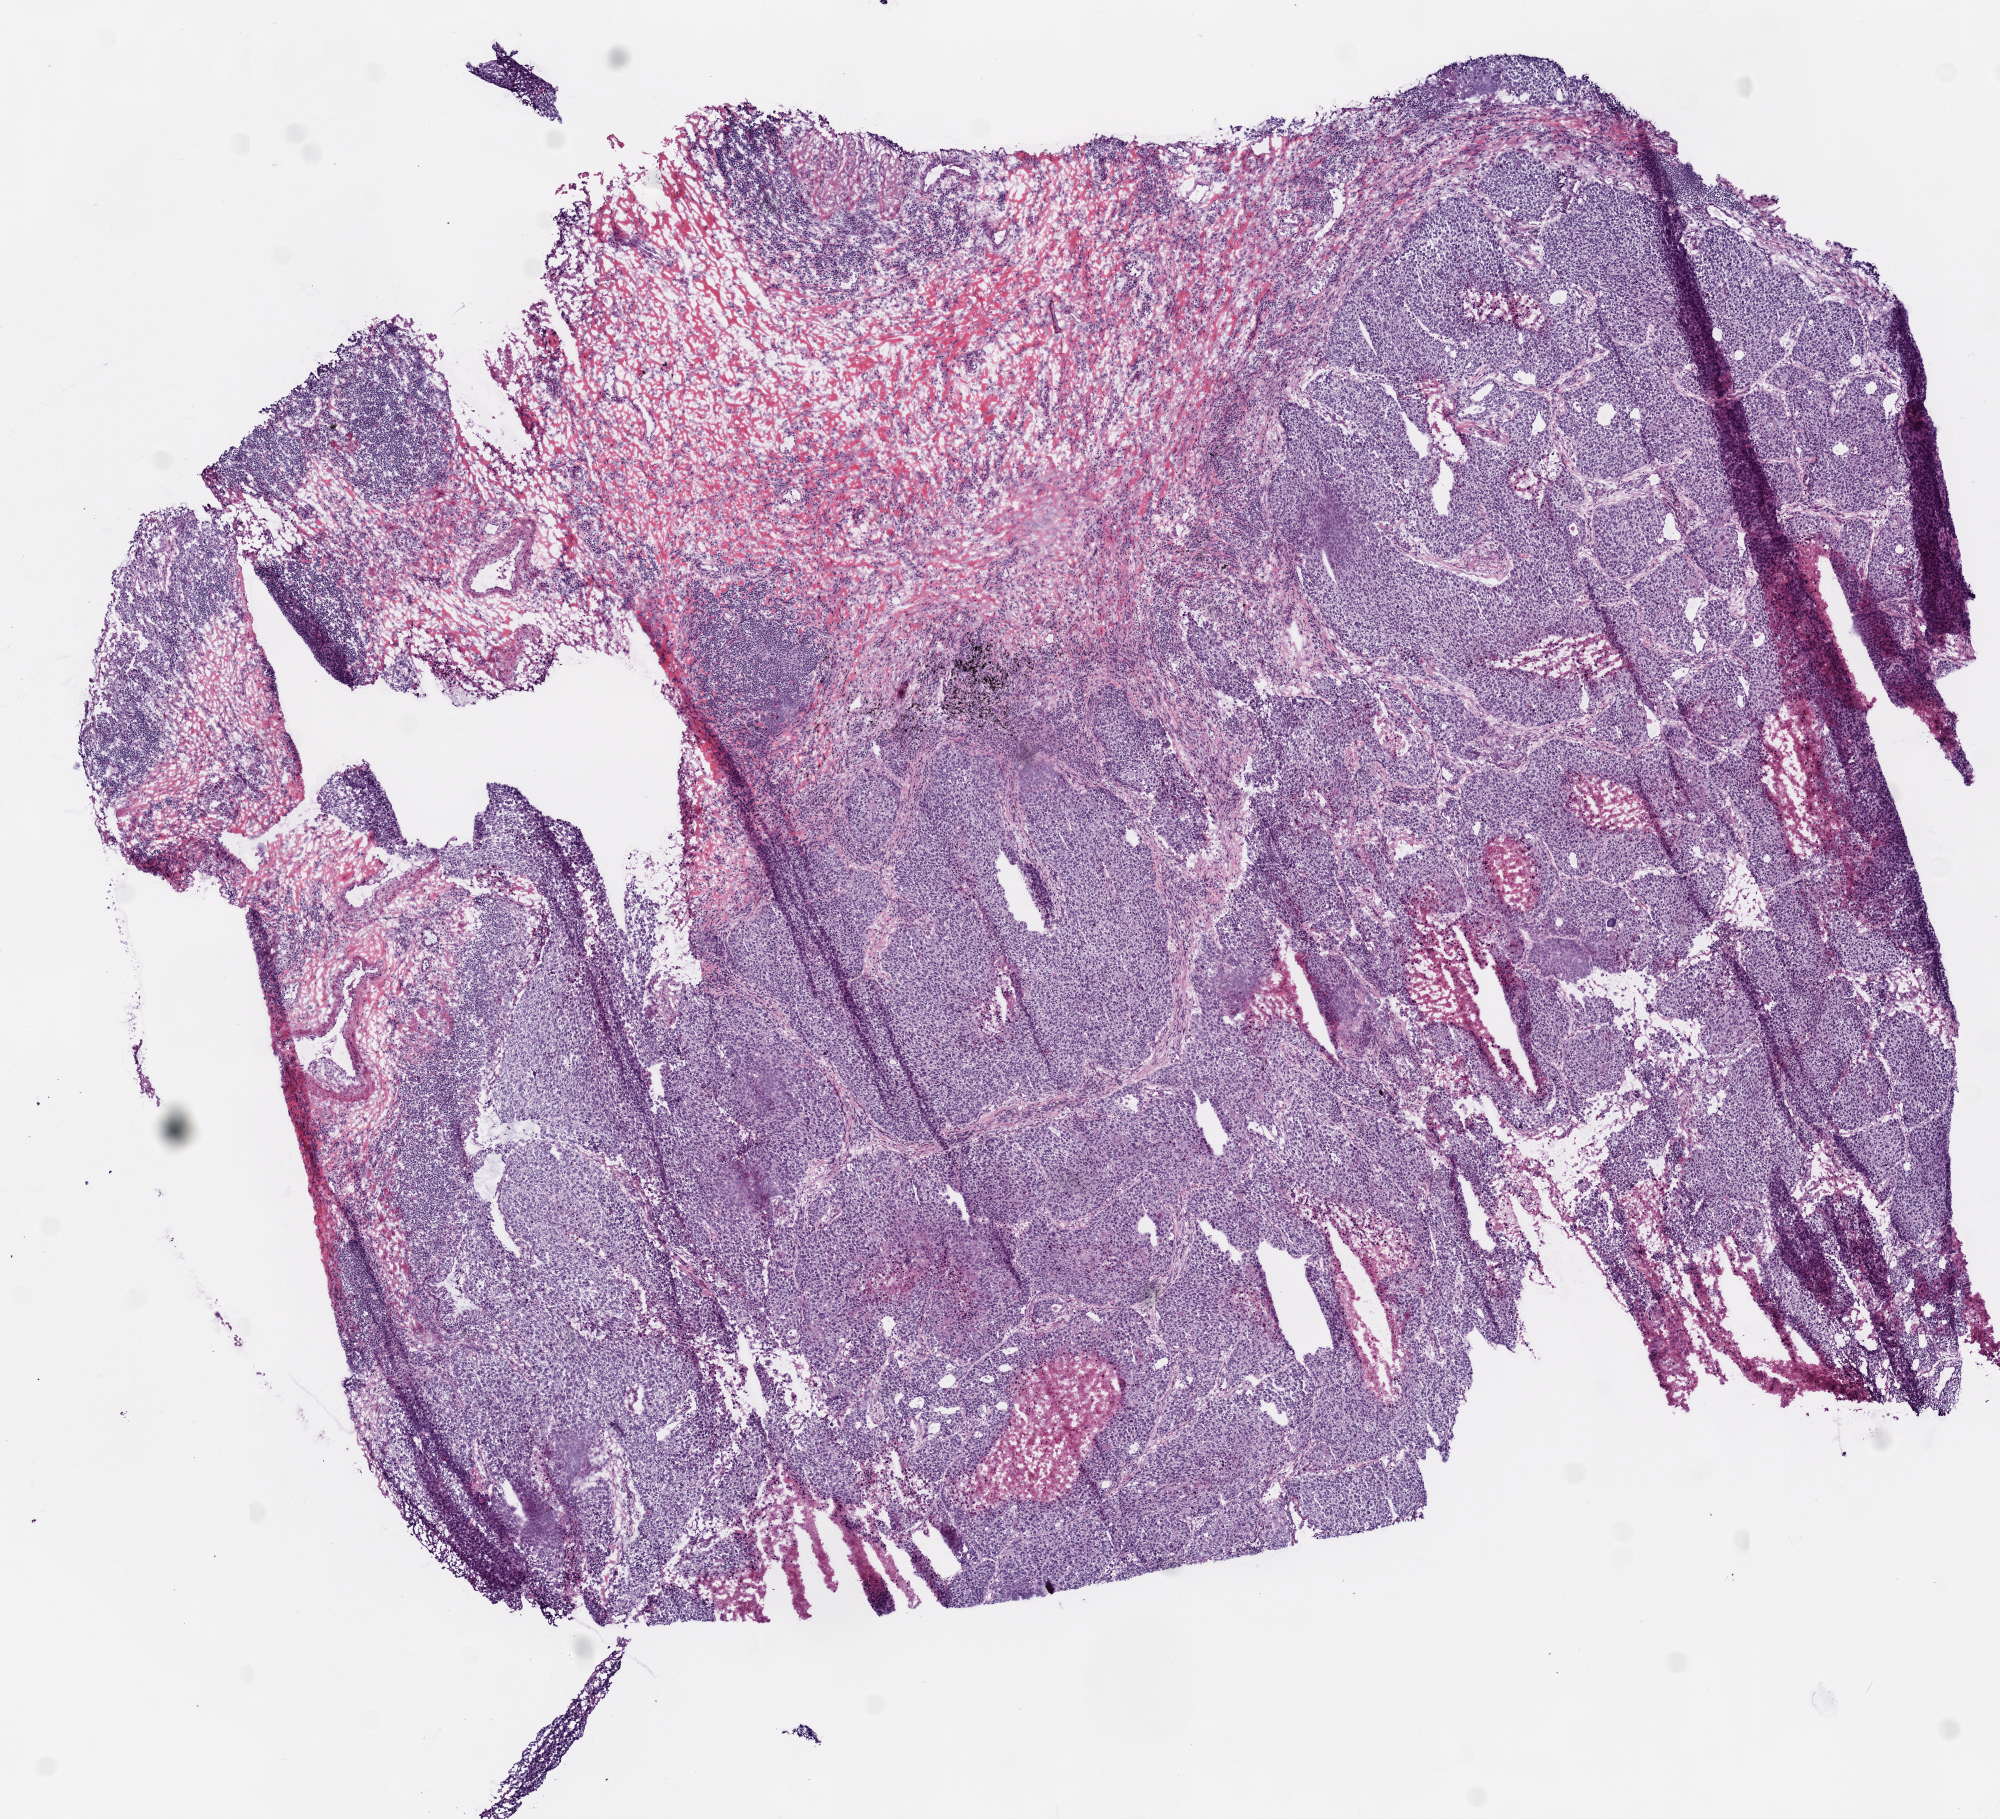
Whole-slide histology image, Hematoxylin and eosin (H&E) stained — shown as a low-resolution overview of the whole scanned area (about 8.0 x 7.3 mm), frozen section from the top of the tissue portion, sample: primary tumour, lung. Male patient; age at initial diagnosis 68 years. Slide review estimates, as recorded: tumour cells 78%, tumour nuclei 70%.
Diagnosis: Squamous cell carcinoma, NOS (middle lobe, lung).